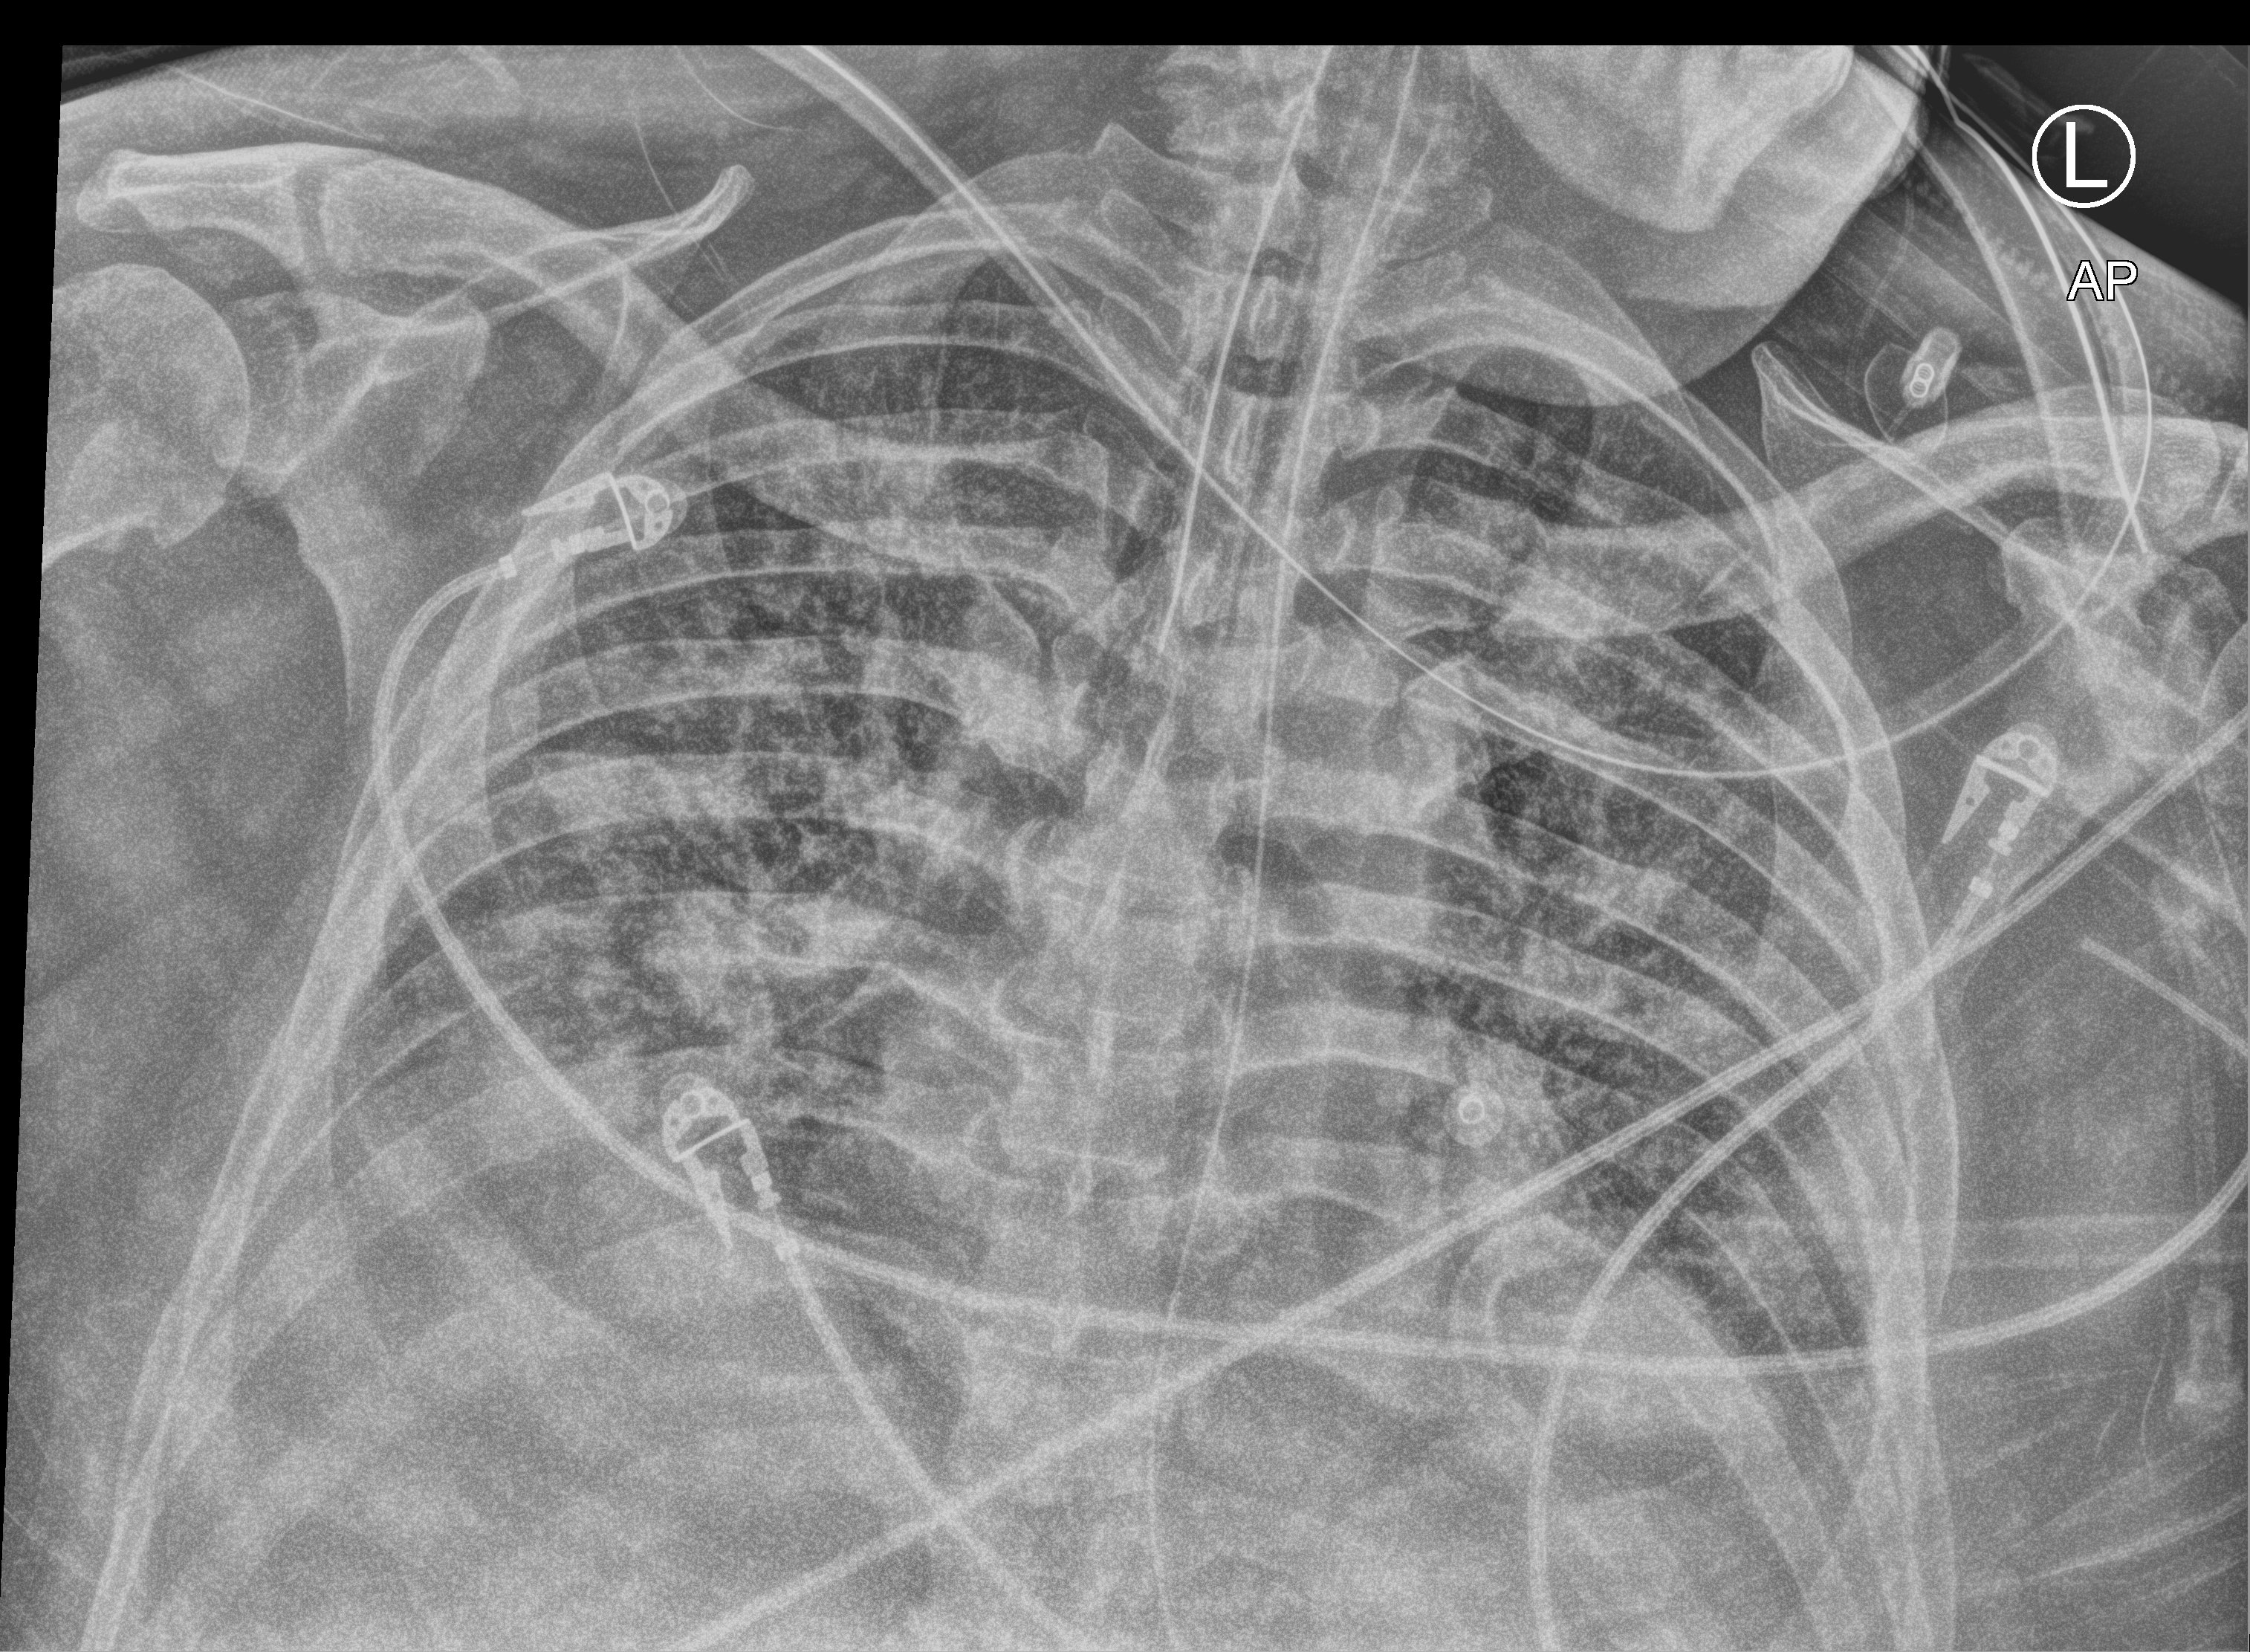
Bedside chest radiograph (computed radiography). Male patient hospitalised with COVID-19, age 18–59 years.
From the hospital-stay record, not from the radiograph (when in the stay this image was taken is not recorded): admitted to intensive care during this hospital stay: yes.